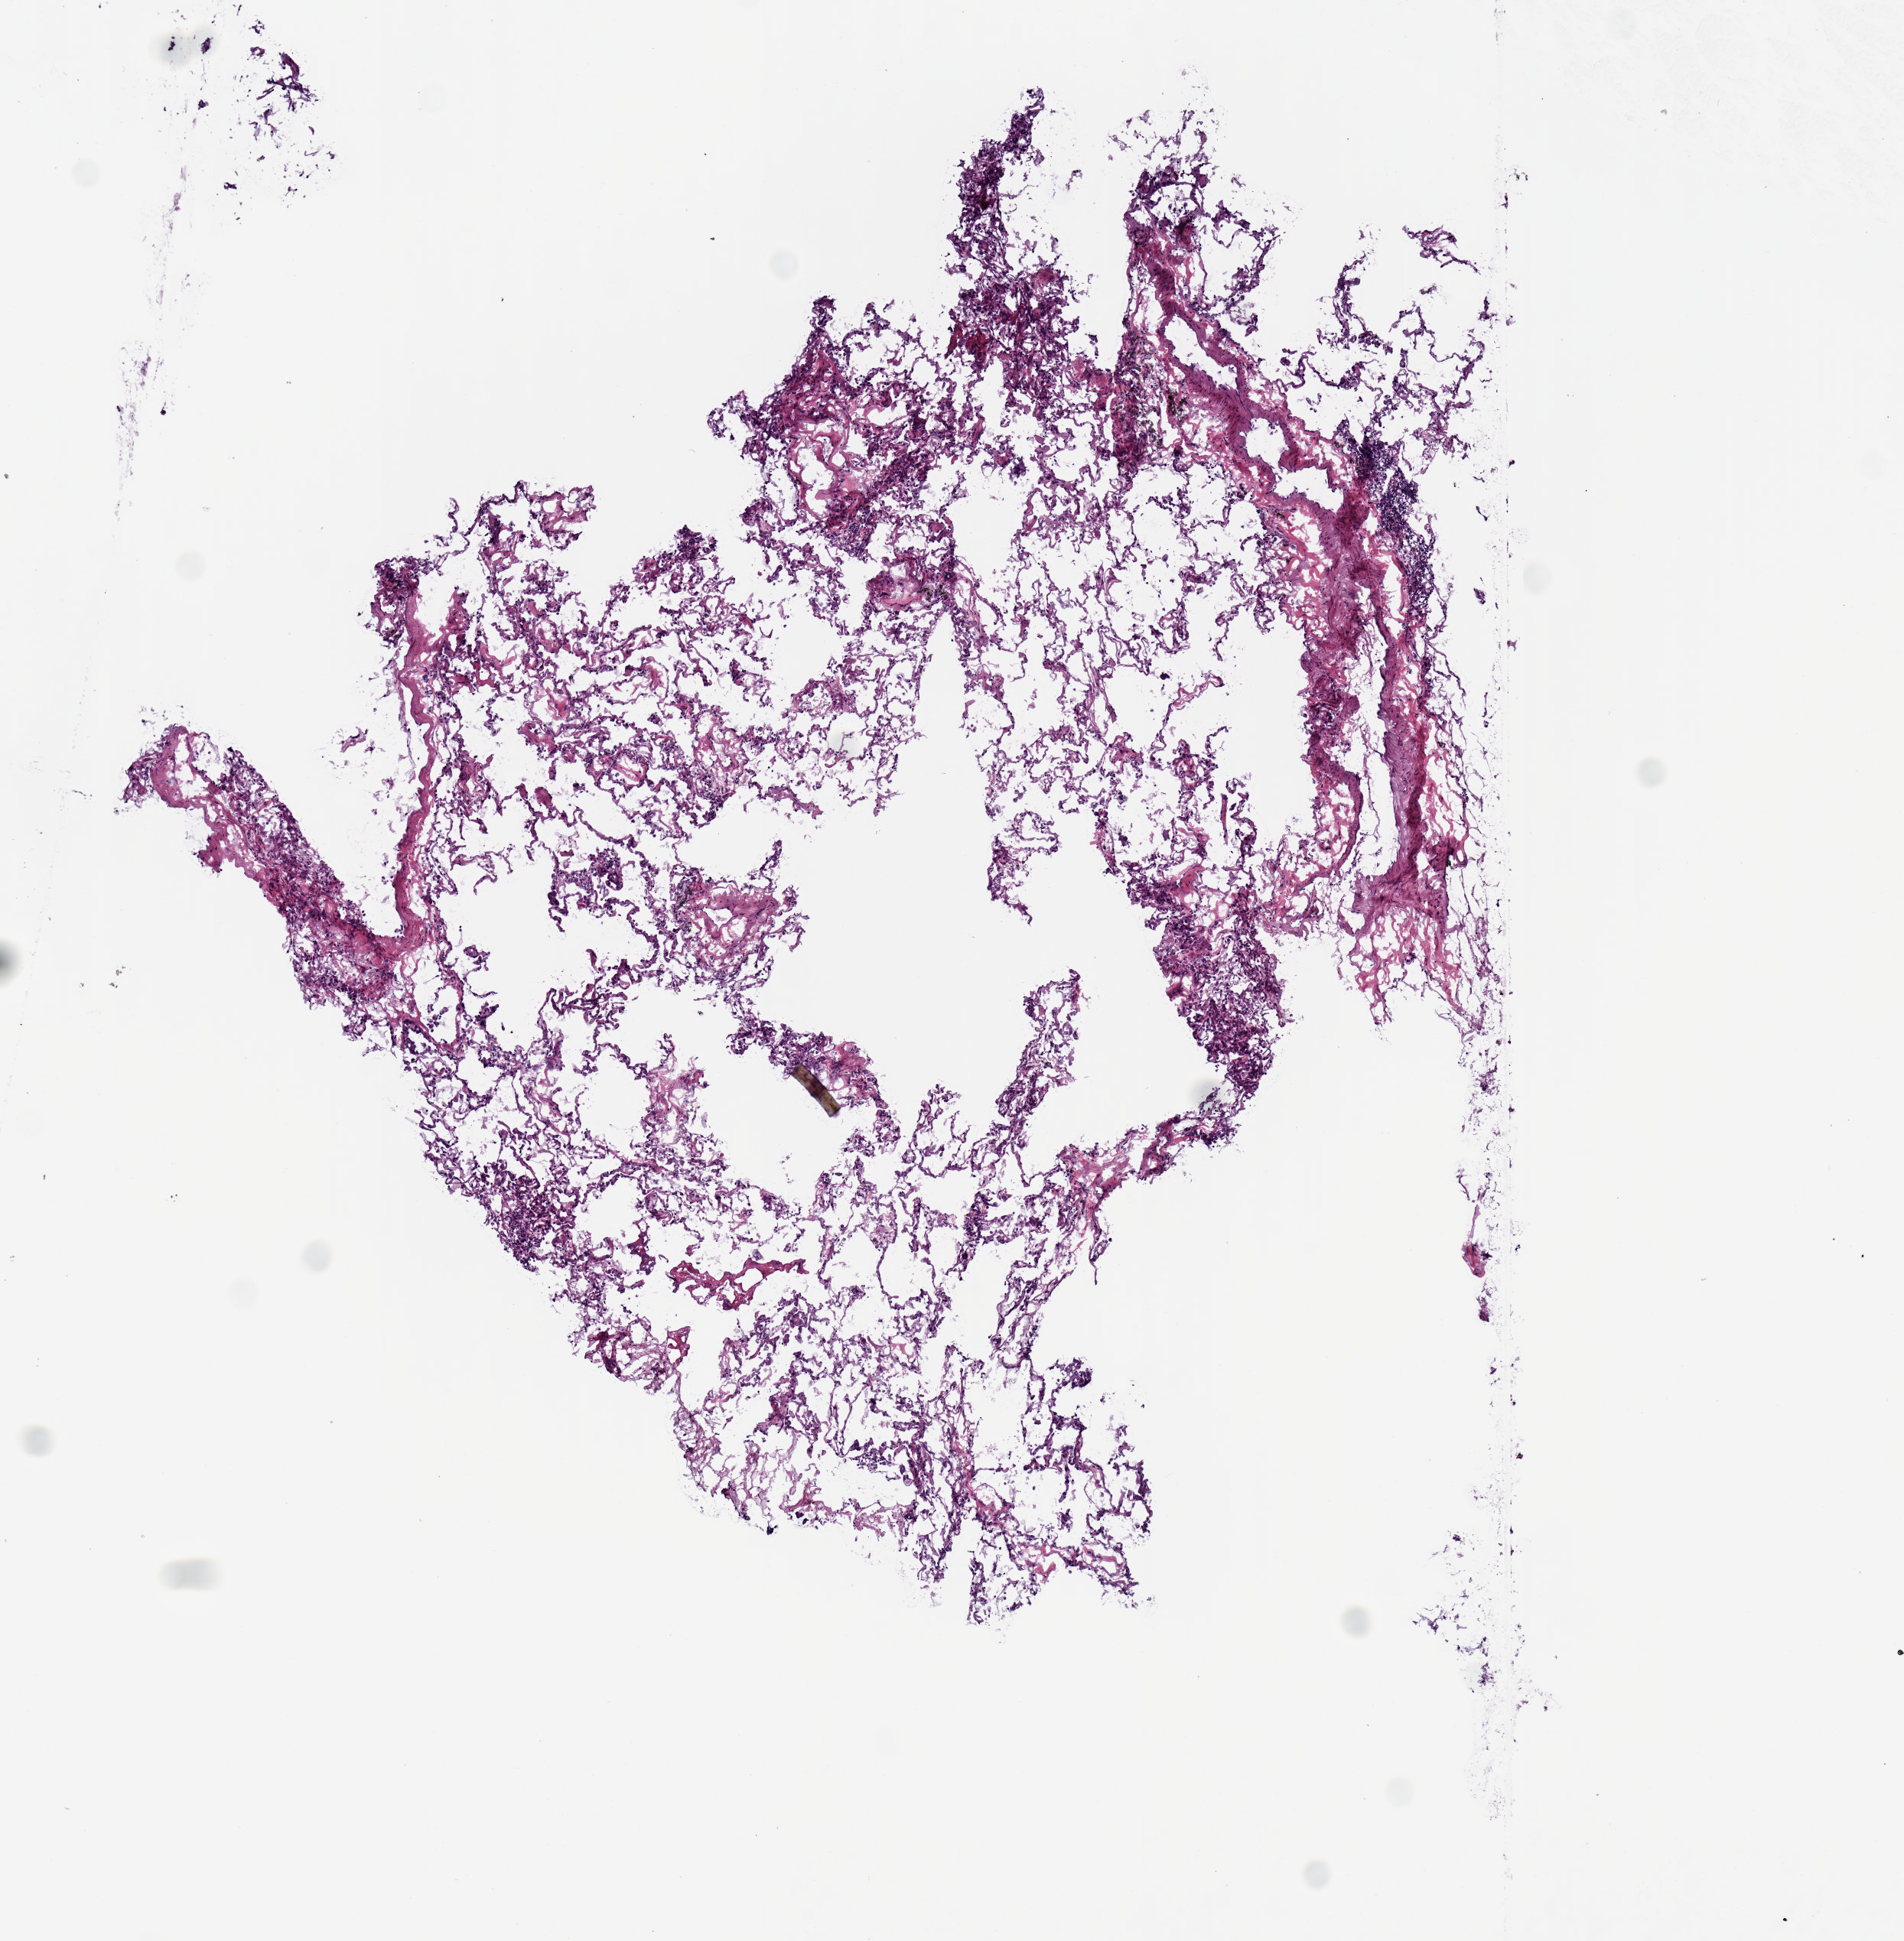
Hematoxylin and eosin (H&E) stained whole-slide image, low-resolution overview of the scanned area, about 4.9 x 5.0 mm (slide scanned at 20x); frozen section; lung, solid tissue normal (non-tumour tissue) sample. Patient: female, age at initial diagnosis 67 years.
* this section: solid tissue normal sample (biorepository sample class)
* patient diagnosis: Papillary adenocarcinoma, NOS